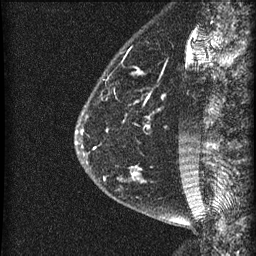
Breast MRI (dynamic contrast-enhanced), one sagittal slice; position 13 of 60 along the scan axis; dynamic contrast-enhanced series, image 2 of 3 at this slice position (ordered by acquisition); 1.5 T; TE 4.2 ms, TR 22.7 ms; 1.5 mm slice thickness; 256 × 256 image matrix, field of view 180 × 180 mm. Female patient, age 48 years. Case-level facts recorded for this patient, not image findings: setting: breast cancer imaged before/during neoadjuvant chemotherapy; receptor status: triple-negative.
Annotated regions visible in this slice (semi-automatically segmented with operator editing):
- analysis volume of interest (the breast-tissue region the enhancement analysis was run in; not a lesion): bounding box (x1, y1, x2, y2) in pixels: (81, 23, 186, 202)
- tumour enhancement mask (voxels above the 90 % enhancement threshold inside the analysis volume of interest): (82, 72, 140, 176)